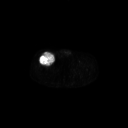
FDG PET of an extremity soft-tissue mass (from a PET/CT study), one axial slice; position 292 of 311 along the scan axis; 128 × 128 image matrix, field of view 700 × 700 mm. Male patient, age 56 years. From the clinical record (not read from this slice): histological type: pleiomorphic leiomyosarcoma; grade: intermediate; site of the primary tumour: right thigh.
Annotated regions visible in this slice (expert contour drawn on MRI and transferred to this co-registered scan by the dataset authors):
- gross tumour volume including surrounding oedema: box from (x=38, y=52) to (x=55, y=66) px
- gross tumour volume (mass): (x=39, y=52)–(x=55, y=66)